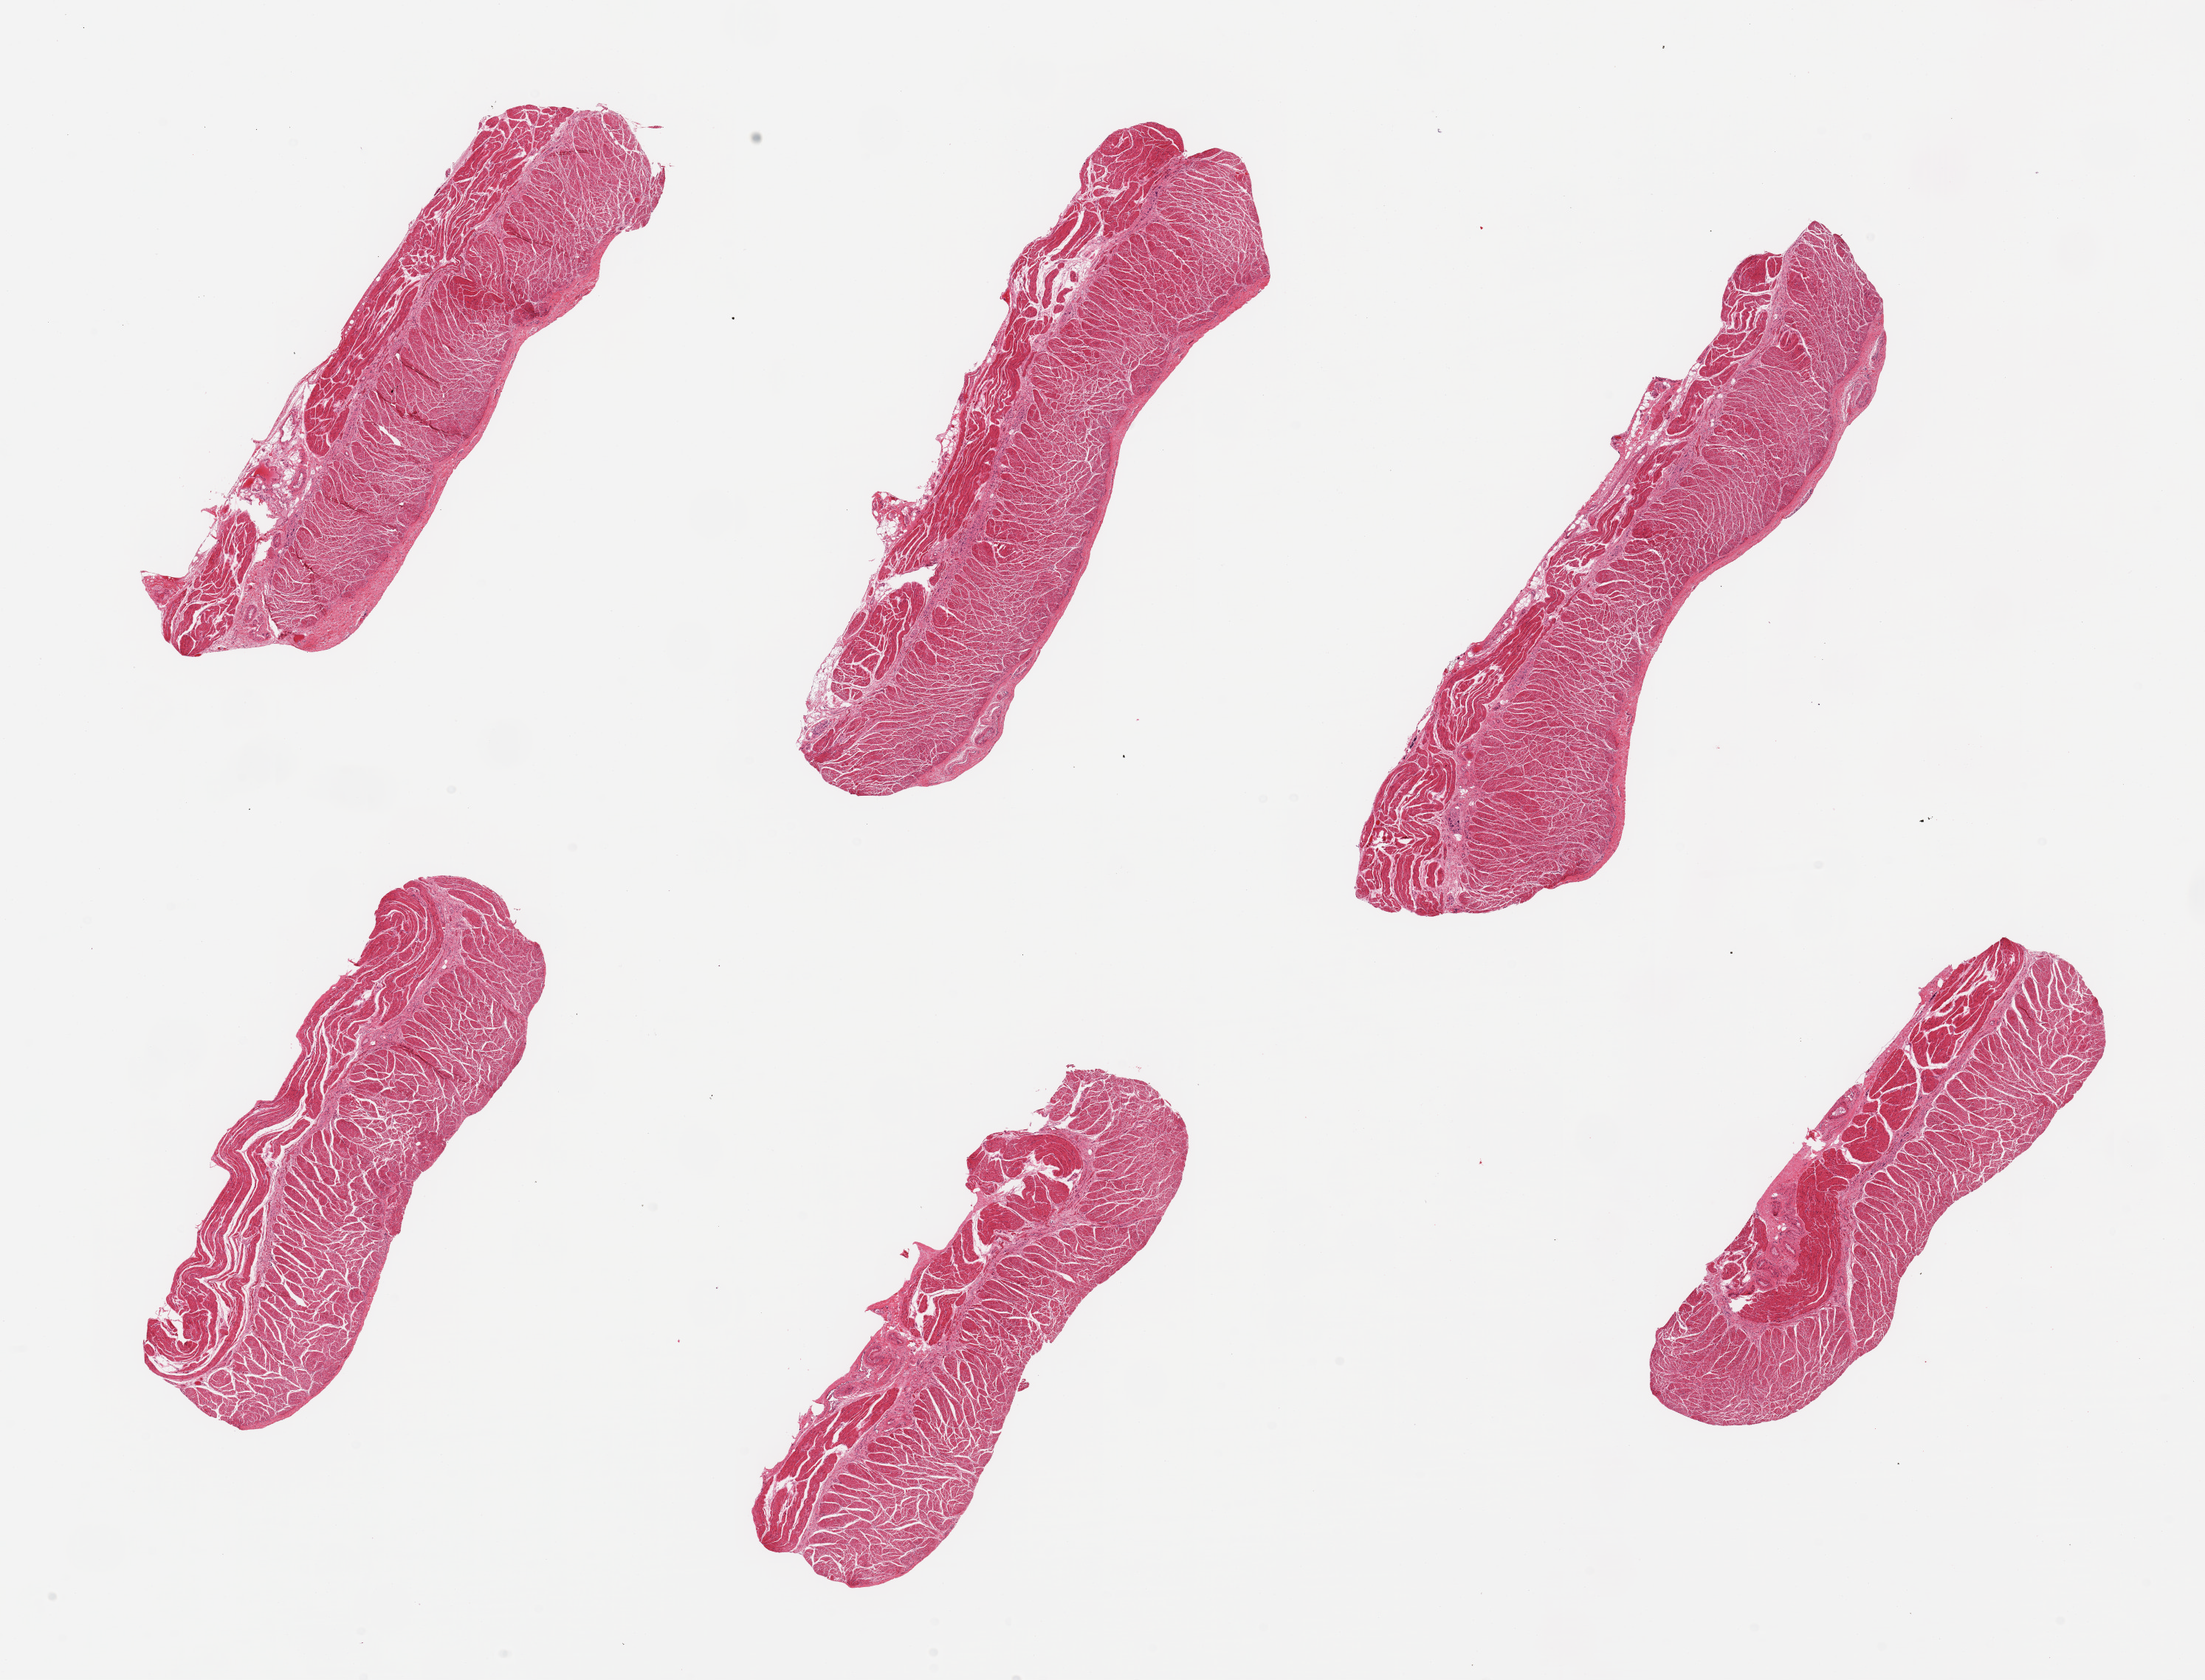
Whole-slide image, hematoxylin and eosin (H&E) stain — low-resolution overview of the scanned area, about 23.6 x 18.0 mm (acquisition: 20x scan), PAXgene-fixed, paraffin-embedded tissue, target tissue: esophageal muscle, tissue donor sample. Donor sex: male.
Reviewer comment on this tissue sample: 6 pieces, confirmed target muscularis.